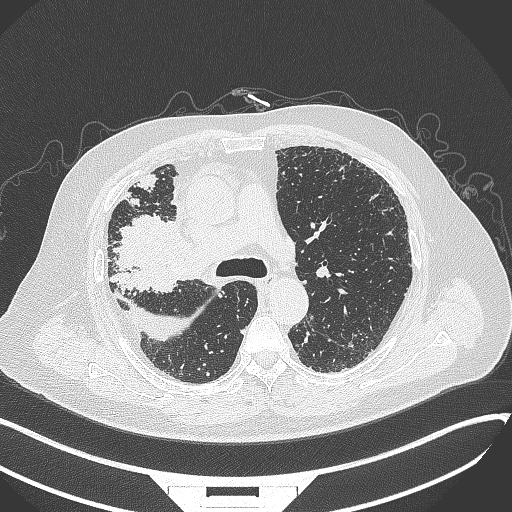
Chest CT, one axial slice; slice 226 of 384 in the series (ordered by position); reconstruction kernel B70f; lung window (W 1500 / L -600 HU); 512 × 512 image matrix. Male patient, age 69 years. From the clinical record (not read from this slice): clinical TNM (as recorded): T4 N3 M1.
Outlined on this slice (bounding box drawn by a radiologist):
- lung tumour (recorded histology: adenocarcinoma): bounding box [x1, y1, x2, y2] px = [106, 212, 191, 303]